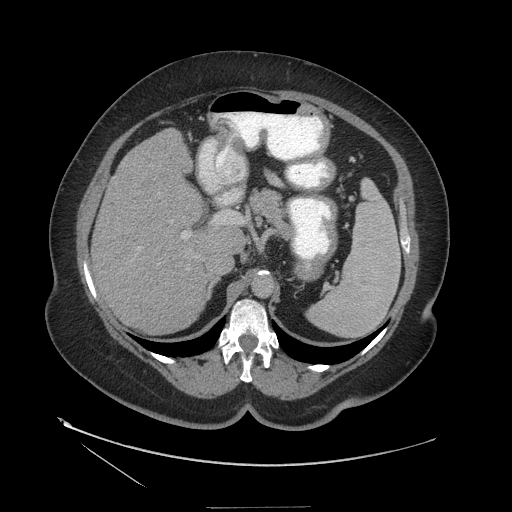
Contrast-enhanced abdominal CT (liver protocol), one axial slice. Position 74 of 127 along the scan axis. Reconstruction kernel STANDARD. Soft-tissue window (W 400 / L 40 HU). 512 × 512 image matrix, field of view 480 × 480 mm. From the clinical record (not read from this slice): diagnosis: hepatocellular carcinoma (patient treated with transarterial chemoembolisation; whether this scan precedes or follows treatment is not stated here); TNM stage (as recorded): Stage-II; Child-Pugh class: A; tumour size: 3 cm.
Outlined on this slice (semi-automatic segmentation, software-assisted and operator-edited):
- liver parenchyma outside the tumour (the mass and vessels are separate outlines, so this box may not span the whole liver): box from (x=92, y=128) to (x=248, y=334) px
- liver vessels: (x=182, y=212)–(x=243, y=238)